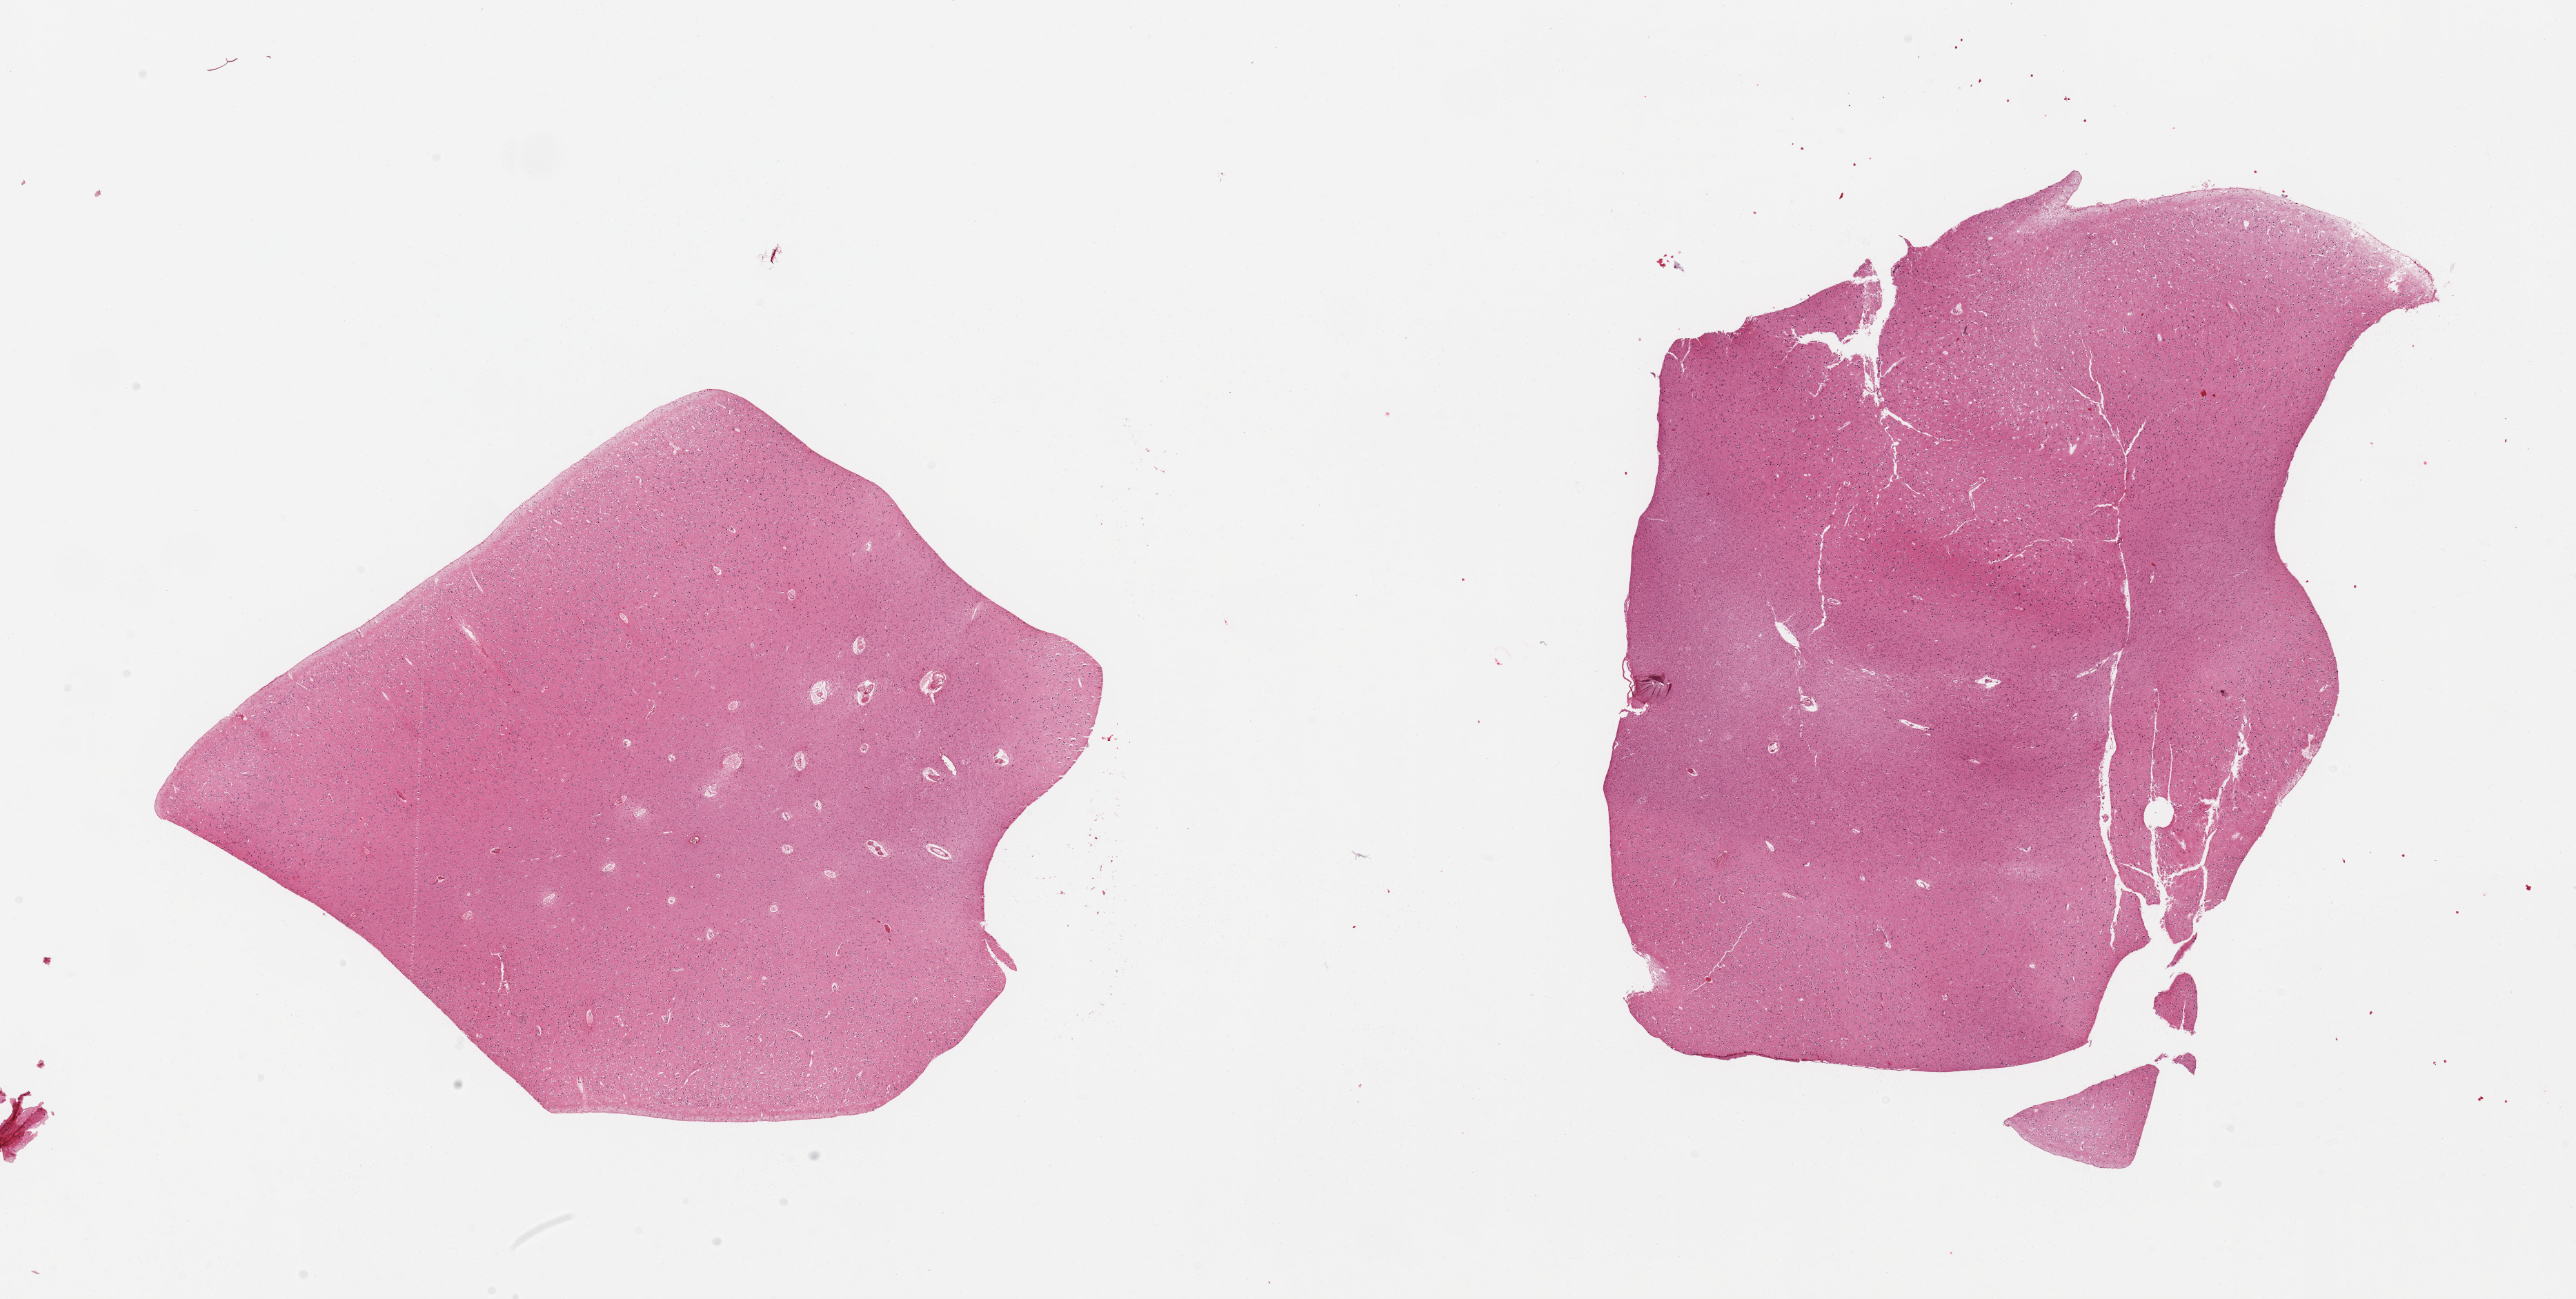
Whole-slide image, hematoxylin and eosin (H&E) stain, a low-resolution overview of the entire scanned area, about 29.5 x 14.9 mm; PAXgene-fixed paraffin-embedded (PFPE) section; section of cerebral cortex (target tissue); donor tissue sample. Donor: male.
Reviewer comment on this tissue sample: 2 pieces; more white matter than usual.